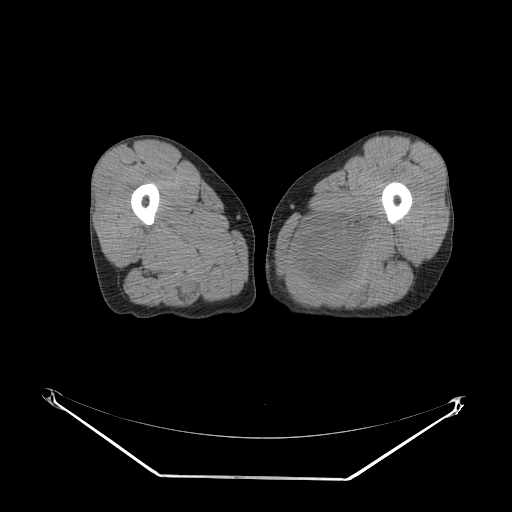
CT of an extremity soft-tissue mass (from a PET/CT study), one axial slice; position 18 of 267 along the scan axis; soft-tissue window (W 400 / L 40 HU); 3.75 mm slice thickness; 512 × 512 image matrix, field of view 500 × 500 mm. Male patient. From the clinical record (not read from this slice): histological type: pleiomorphic liposarcoma; grade: high; site of the primary tumour: left thigh.
Annotated regions visible in this slice (expert contour drawn on MRI and transferred to this co-registered scan by the dataset authors):
- gross tumour volume including surrounding oedema: bounding box <297,206,382,295> (left, top, right, bottom; pixels)
- gross tumour volume (mass): <304,228,366,289>